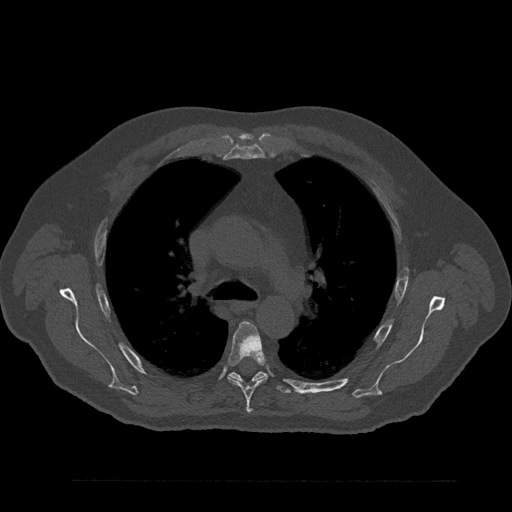
CT including the spine, one axial slice. Position 591 of 797 along the scan axis. 120 kVp. Bone window (W 1800 / L 400 HU). 0.5 mm slice thickness. 512 × 512 image matrix, field of view 430 × 430 mm. Patient: male, 61 years. Case-level facts recorded for this patient, not image findings: primary cancer: prostate.
Structures marked on this image (semi-automatically segmented with operator editing):
- T5 vertebra: bounding box (x1, y1, x2, y2) in pixels: (227, 322, 267, 414)
- T6 vertebra: (228, 364, 291, 394)